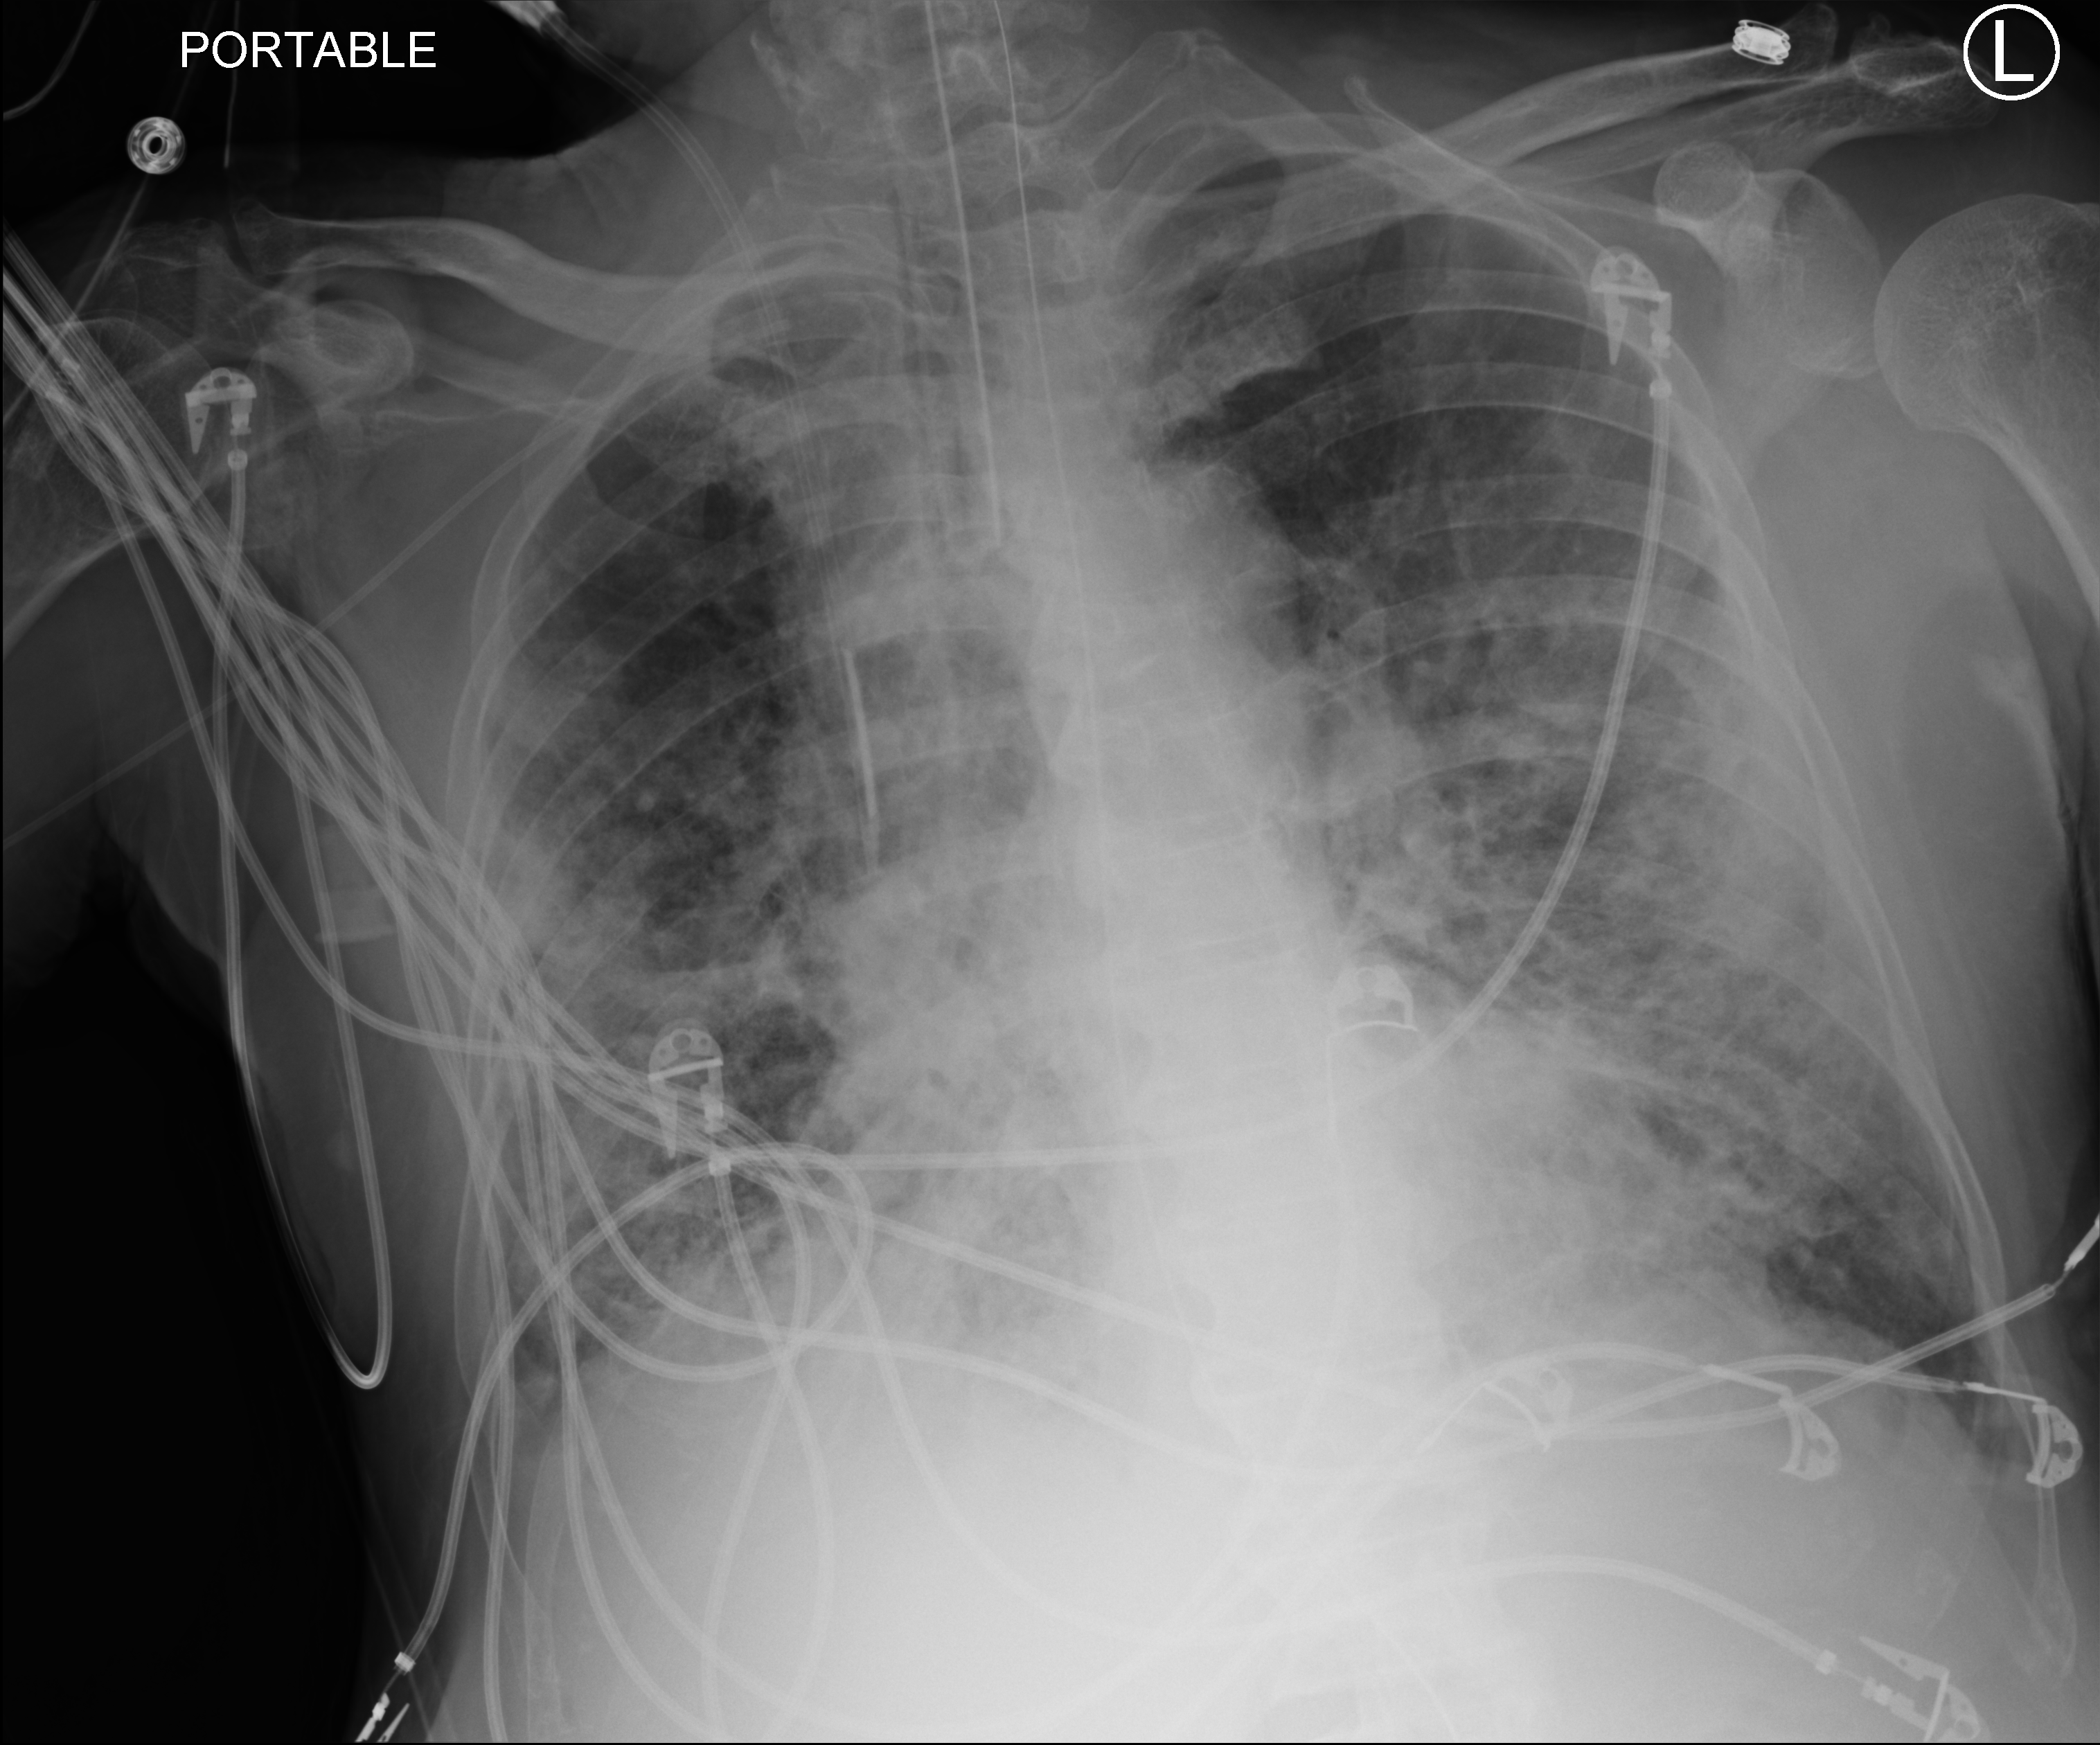
Chest X-ray (portable), anteroposterior (AP) projection. Patient hospitalised with COVID-19; male, aged 60–74 years.
Admission-level facts for this patient (not findings on this image; timing relative to this image not recorded):
- admitted to intensive care during this hospital stay: yes